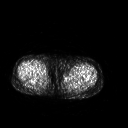
FDG PET of an extremity soft-tissue mass (from a PET/CT study), one axial slice; 3.27 mm slice thickness; 128 × 128 image matrix, field of view 500 × 500 mm. Female patient, age 42 years. From the clinical record (not read from this slice): histological type: pleiomorphic leiomyosarcoma; grade: intermediate; site of the primary tumour: left thigh.
Outlined on this slice (expert contour drawn on MRI and transferred to this co-registered scan by the dataset authors):
- gross tumour volume including surrounding oedema: bounding box [x1, y1, x2, y2] px = [65, 72, 81, 79]